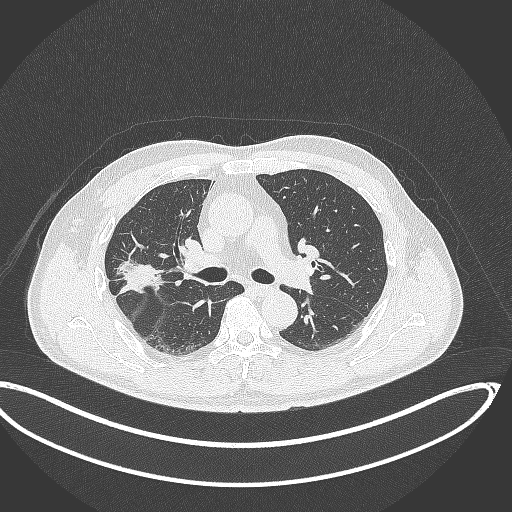
Chest CT, one axial slice; position 208 of 391 along the scan axis; reconstruction kernel B70f; 120 kVp; lung window (W 1500 / L -600 HU); 512 × 512 image matrix. Patient: male, 63 years. Case-level facts recorded for this patient, not image findings: clinical TNM (as recorded): T1c N0 M0.
Structures marked on this image (bounding box drawn by a radiologist):
- lung tumour (recorded histology: adenocarcinoma): bounding box [x1, y1, x2, y2] px = [115, 250, 166, 301]